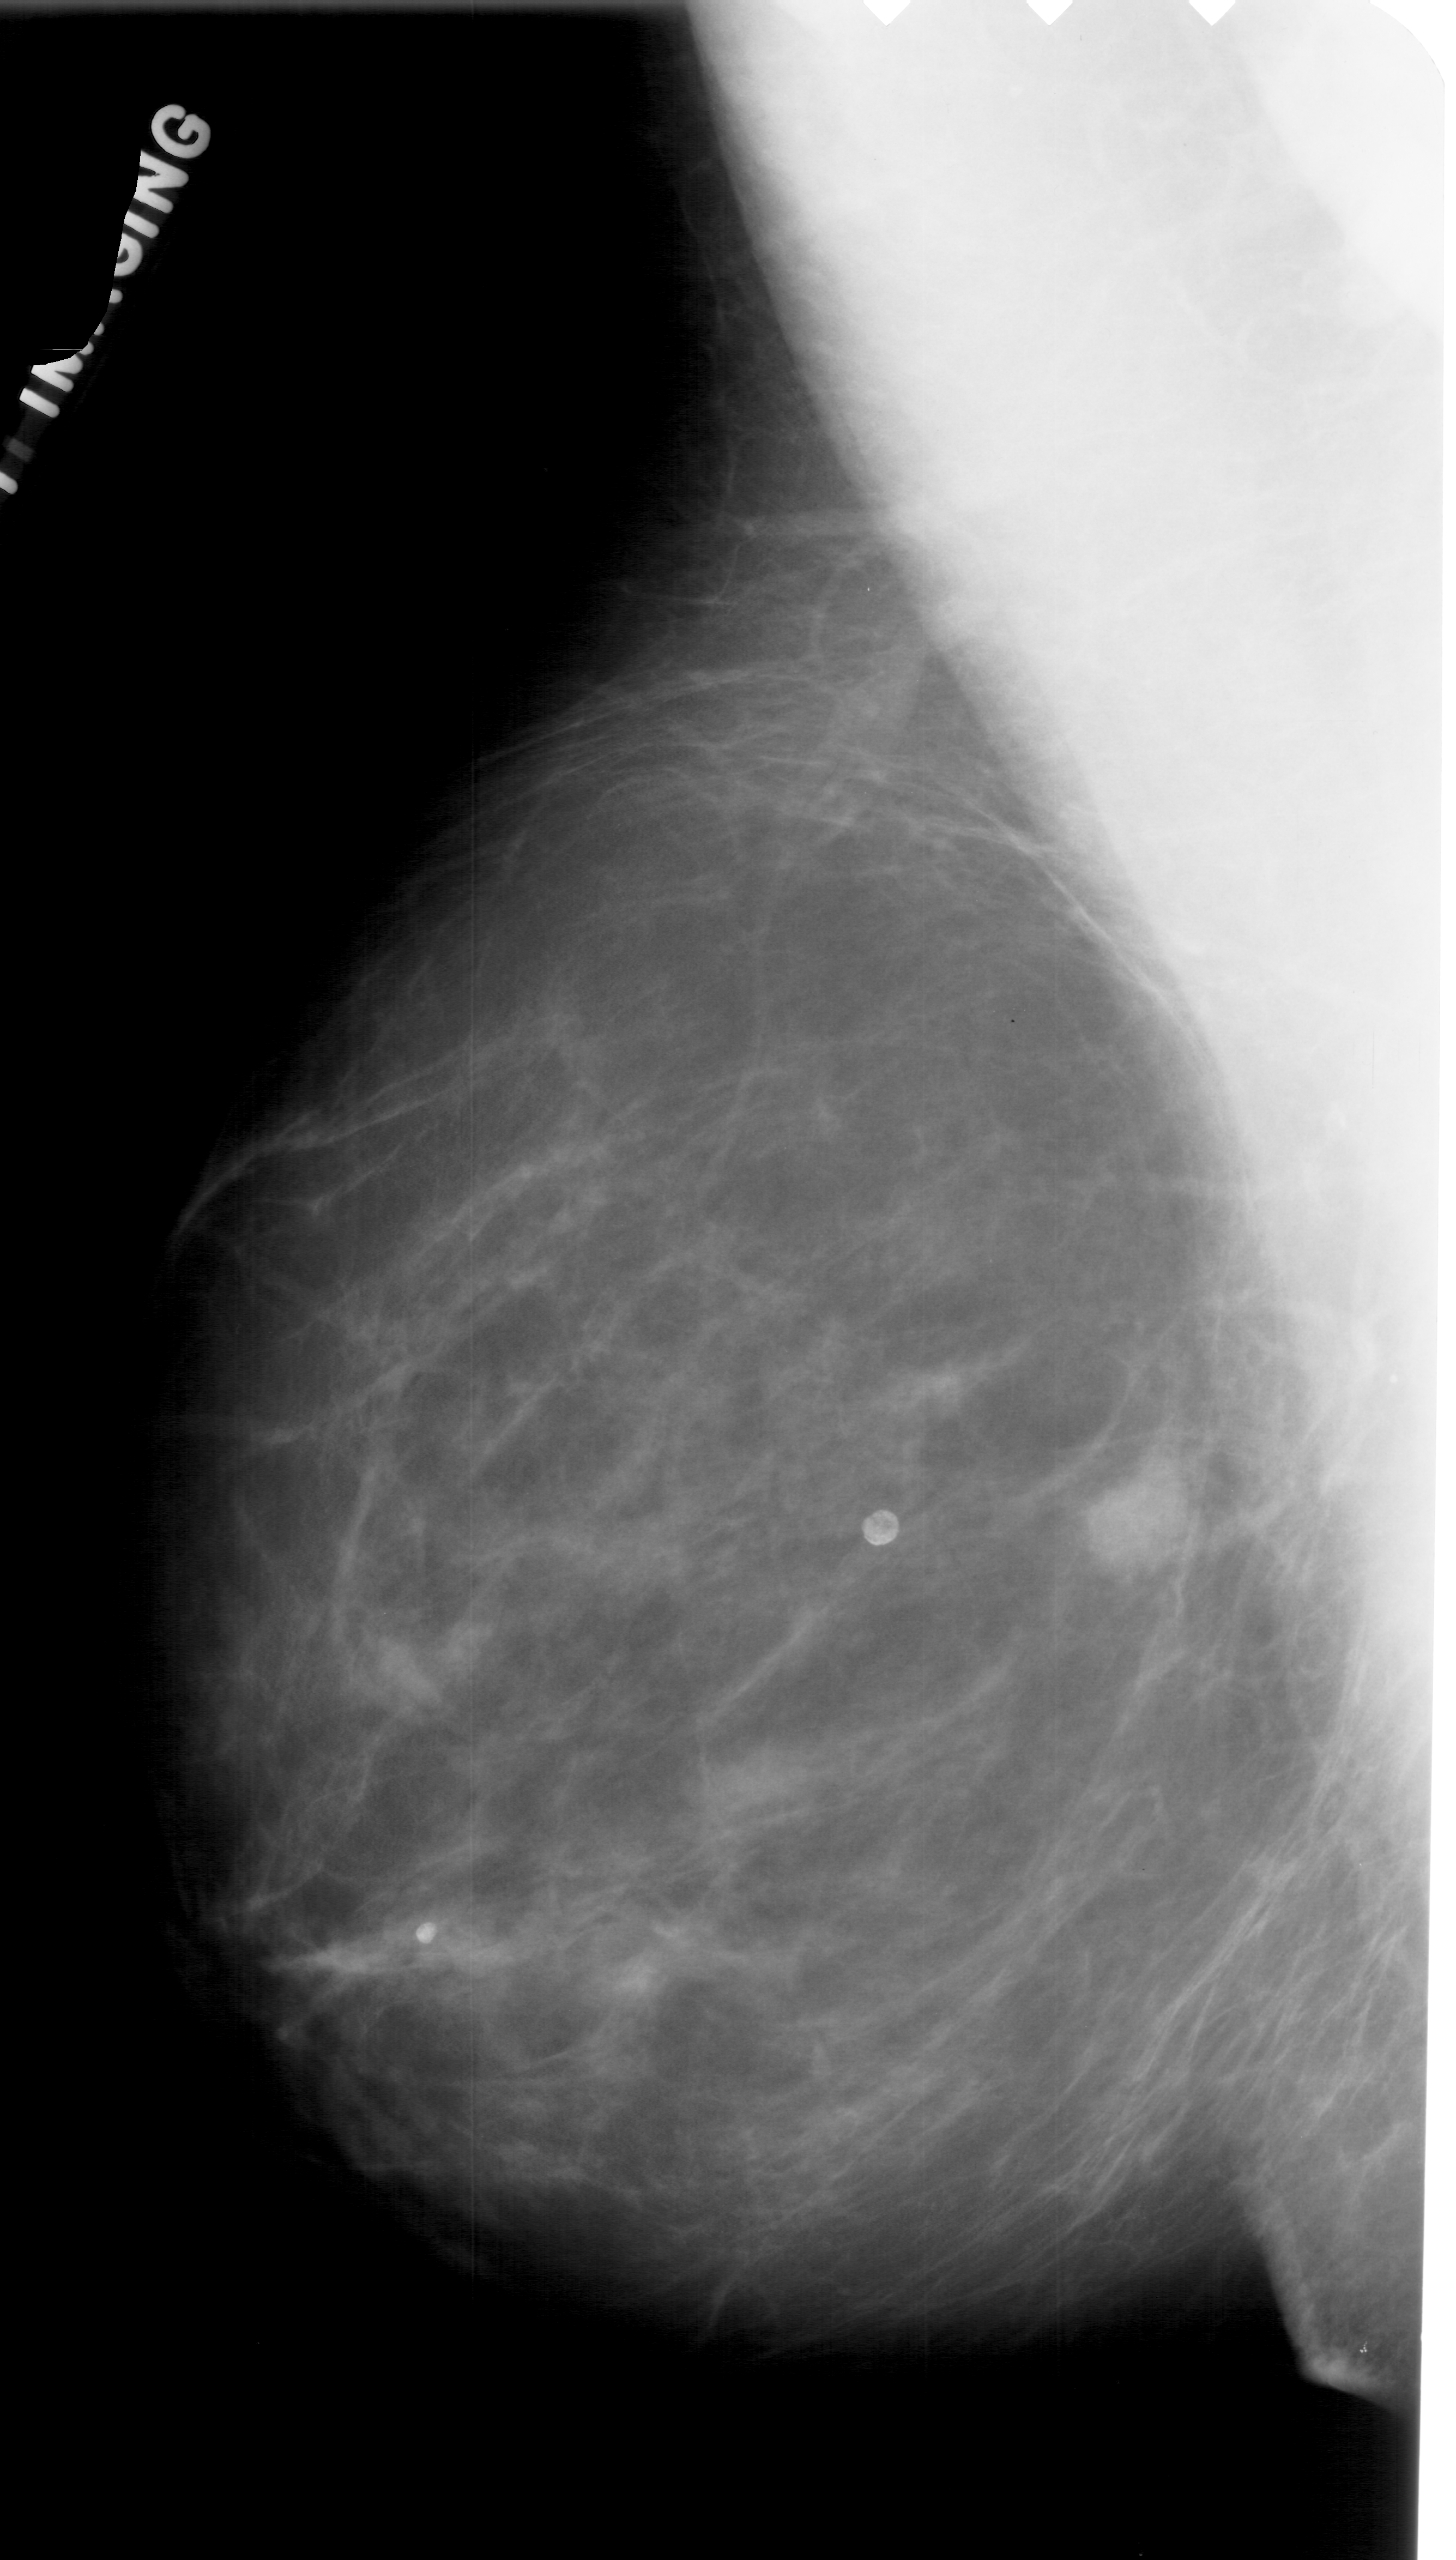
Scanned film-screen mammogram; left breast; MLO view; BI-RADS breast density category 2 (scale 1–4); 1456 × 2560 image matrix.
Expert-marked regions of interest on this film, with their recorded descriptors:
- mass, shape lobulated, margins obscured; BI-RADS assessment category 4; pathology (as recorded): benign: box from (x=1073, y=1463) to (x=1189, y=1582) px